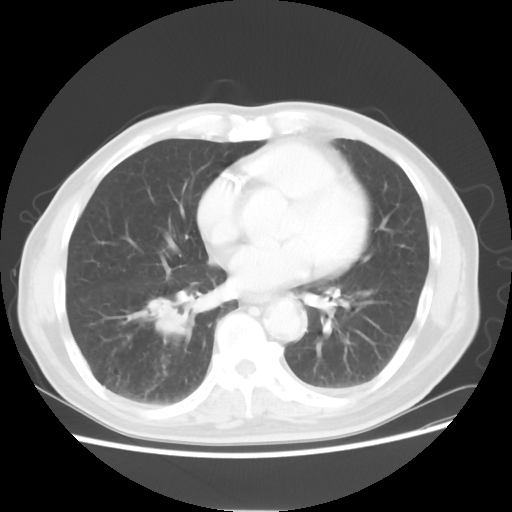
Chest CT, one axial slice; position 25 of 58 along the scan axis; 120 kVp; lung window (W 1500 / L -600 HU); 512 × 512 image matrix, field of view 360 × 360 mm. Patient: male, 74 years. Case-level facts recorded for this patient, not image findings: clinical TNM (as recorded): T1c N1 M1.
Outlined on this slice (rectangle marked by the reading radiologist):
- lung tumour (recorded histology: adenocarcinoma): bounding box (x1, y1, x2, y2) in pixels: (122, 293, 201, 350)